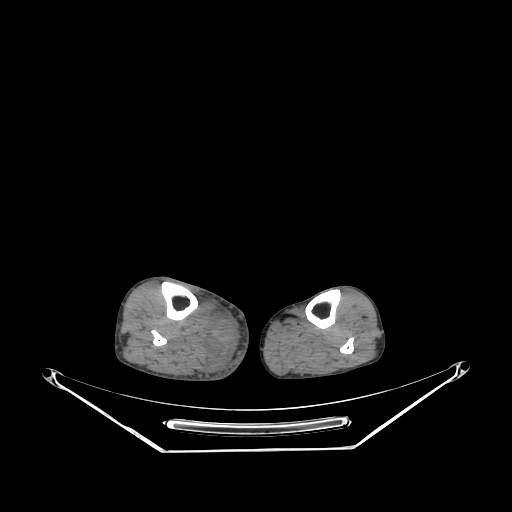
CT of an extremity soft-tissue mass (from a PET/CT study), one axial slice; slice 126 of 267 in the series (ordered by position); reconstruction kernel SOFT; 140 kVp; soft-tissue window (W 400 / L 40 HU); 3.75 mm slice thickness; 512 × 512 image matrix, field of view 500 × 500 mm. Male patient. From the clinical record (not read from this slice): histological type: pleiomorphic liposarcoma; grade: high; site of the primary tumour: right calf.
Outlined on this slice (expert contour drawn on MRI and transferred to this co-registered scan by the dataset authors):
- gross tumour volume including surrounding oedema: box from (x=206, y=308) to (x=238, y=371) px
- gross tumour volume (mass): (x=210, y=320)–(x=232, y=344)